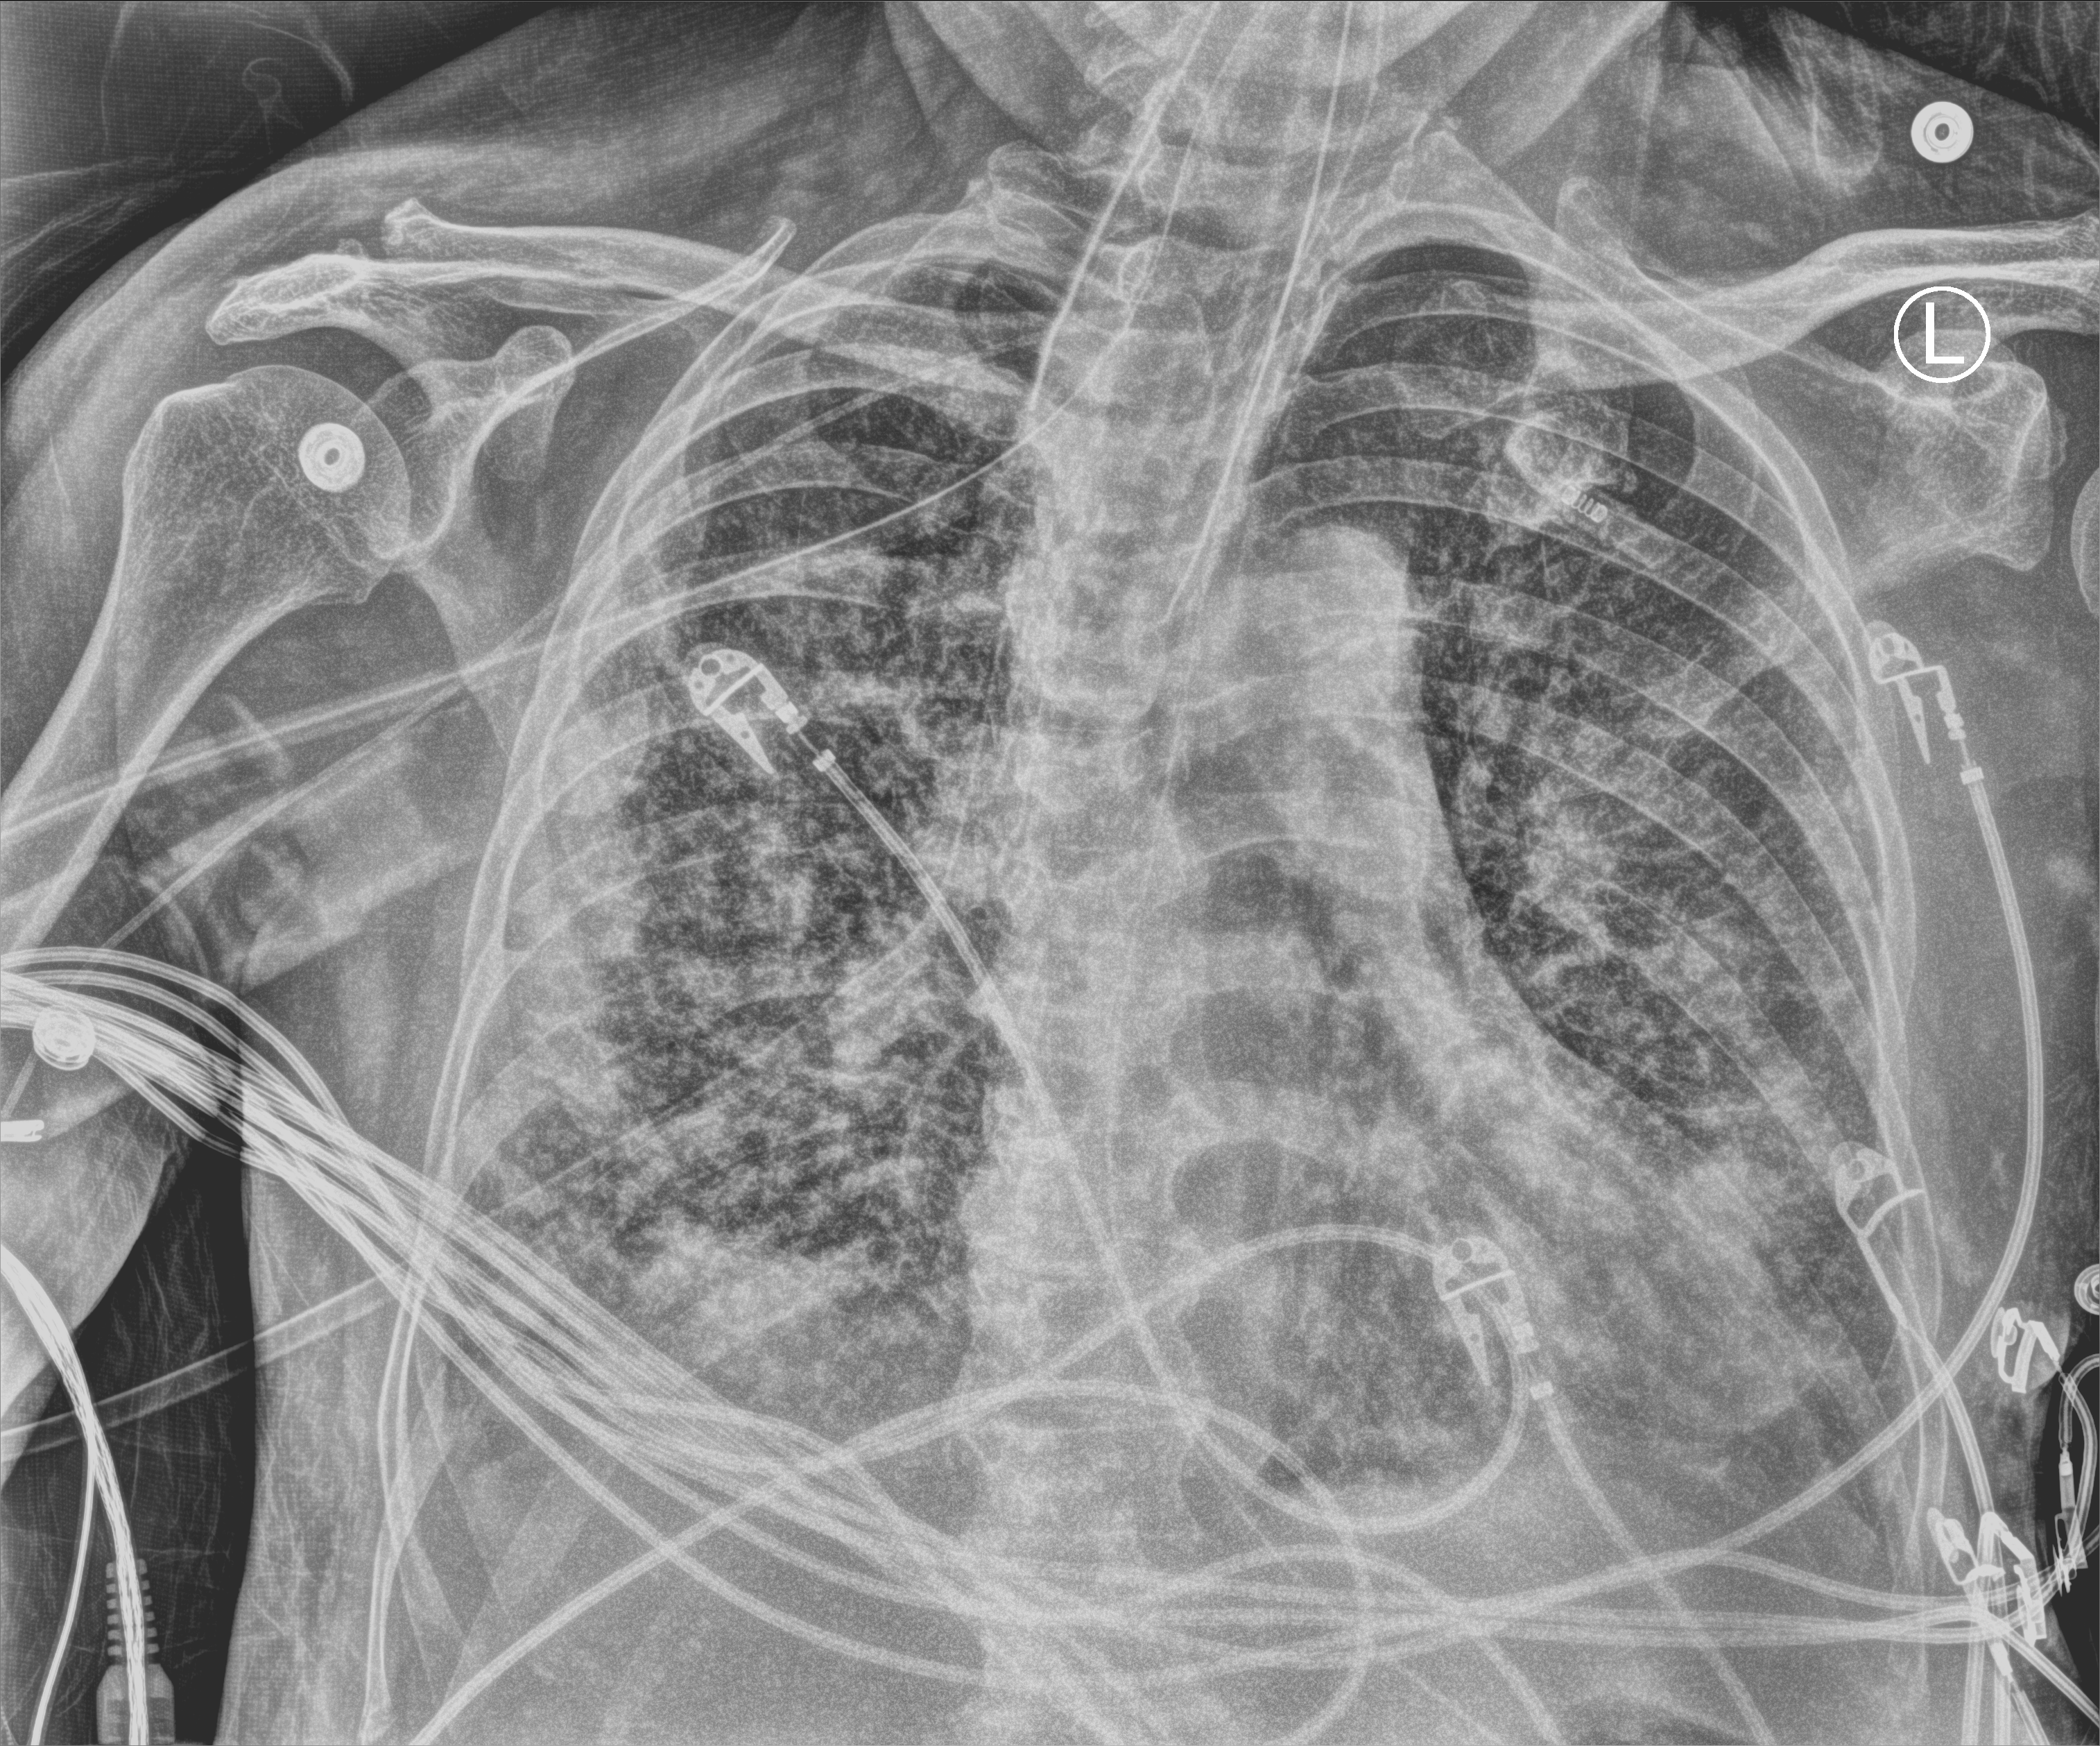
Chest X-ray (portable); anteroposterior (AP) projection. Male patient hospitalised with COVID-19, age 60–74 years.
Hospital-stay facts (about this admission, not read from this image; timing relative to this image not recorded): admitted to intensive care during this hospital stay: yes.